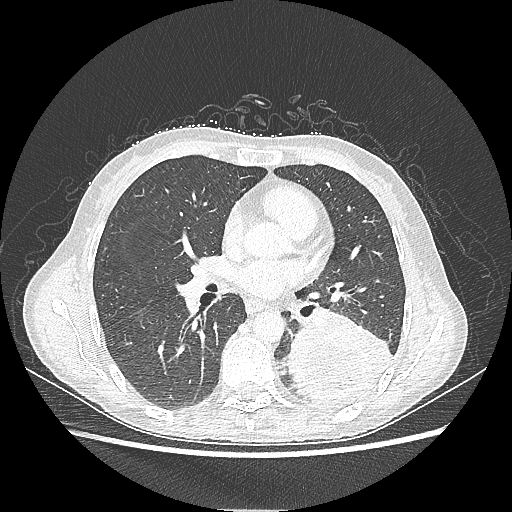
Chest CT, one axial slice; position 114 of 220 along the scan axis; reconstruction kernel LUNG; 80 kVp; lung window (W 1500 / L -600 HU); 1.25 mm slice thickness; 512 × 512 image matrix, field of view 360 × 360 mm. Patient: female, 53 years. Case-level facts recorded for this patient, not image findings: clinical TNM (as recorded): T3 N0 M0.
Outlined on this slice (bounding box drawn by a radiologist):
- lung tumour (recorded histology: adenocarcinoma): bounding box [x1, y1, x2, y2] px = [284, 309, 394, 417]